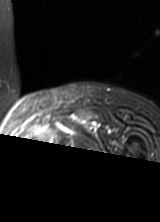
MRI of an extremity soft-tissue mass, one axial slice; T2-weighted fat-saturated; MR volume resampled by the dataset authors to the PET/CT grid (not the native acquisition matrix); 160 × 222 image matrix, field of view 156 × 217 mm. Female patient. From the clinical record (not read from this slice): histological type: pleomorphic leiomyosarcoma; grade: high; site of the primary tumour: left thigh.
Annotated regions visible in this slice (expert contour drawn on MRI and transferred to this co-registered scan by the dataset authors):
- gross tumour volume including surrounding oedema: bounding box [x1, y1, x2, y2] px = [31, 127, 56, 153]